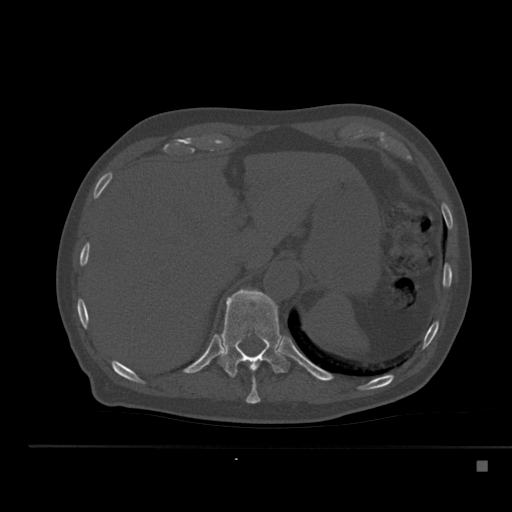
CT including the spine, one axial slice; position 252 of 517 along the scan axis; reconstruction kernel Br40s; 120 kVp; bone window (W 1800 / L 400 HU); 1.5 mm slice thickness; 512 × 512 image matrix, field of view 408 × 408 mm. Patient: male, 70 years. From the clinical record (not read from this slice): primary cancer: renal.
Structures marked on this image (semi-automatically segmented with operator editing):
- T10 vertebra: bounding box <246,360,260,404> (left, top, right, bottom; pixels)
- T11 vertebra: <219,289,289,378>